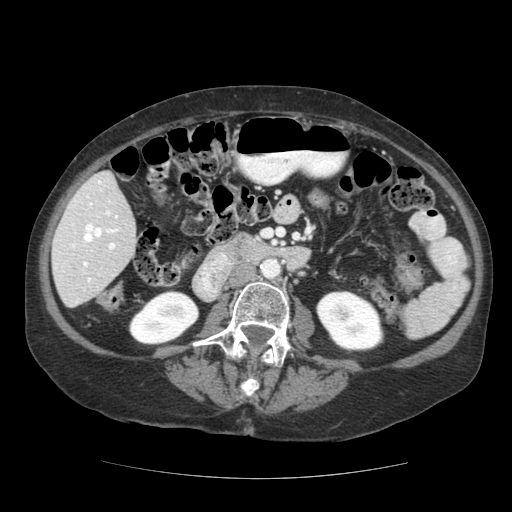
Contrast-enhanced abdominal CT (liver protocol), one axial slice; position 46 of 111 along the scan axis; reconstruction kernel STANDARD; soft-tissue window (W 400 / L 40 HU); 2.5 mm slice thickness; 512 × 512 image matrix. Case-level facts recorded for this patient, not image findings: diagnosis: hepatocellular carcinoma (patient treated with transarterial chemoembolisation; whether this scan precedes or follows treatment is not stated here); TNM stage (as recorded): Stage-I; Child-Pugh class: A; tumour differentiation: moderately-poorly differentiated; tumour nodularity: uninodular.
Annotated regions visible in this slice (semi-automatically segmented with operator editing):
- liver parenchyma outside the tumour (the mass and vessels are separate outlines, so this box may not span the whole liver): bounding box [x1, y1, x2, y2] px = [52, 172, 136, 306]
- liver vessels: [55, 180, 120, 303]